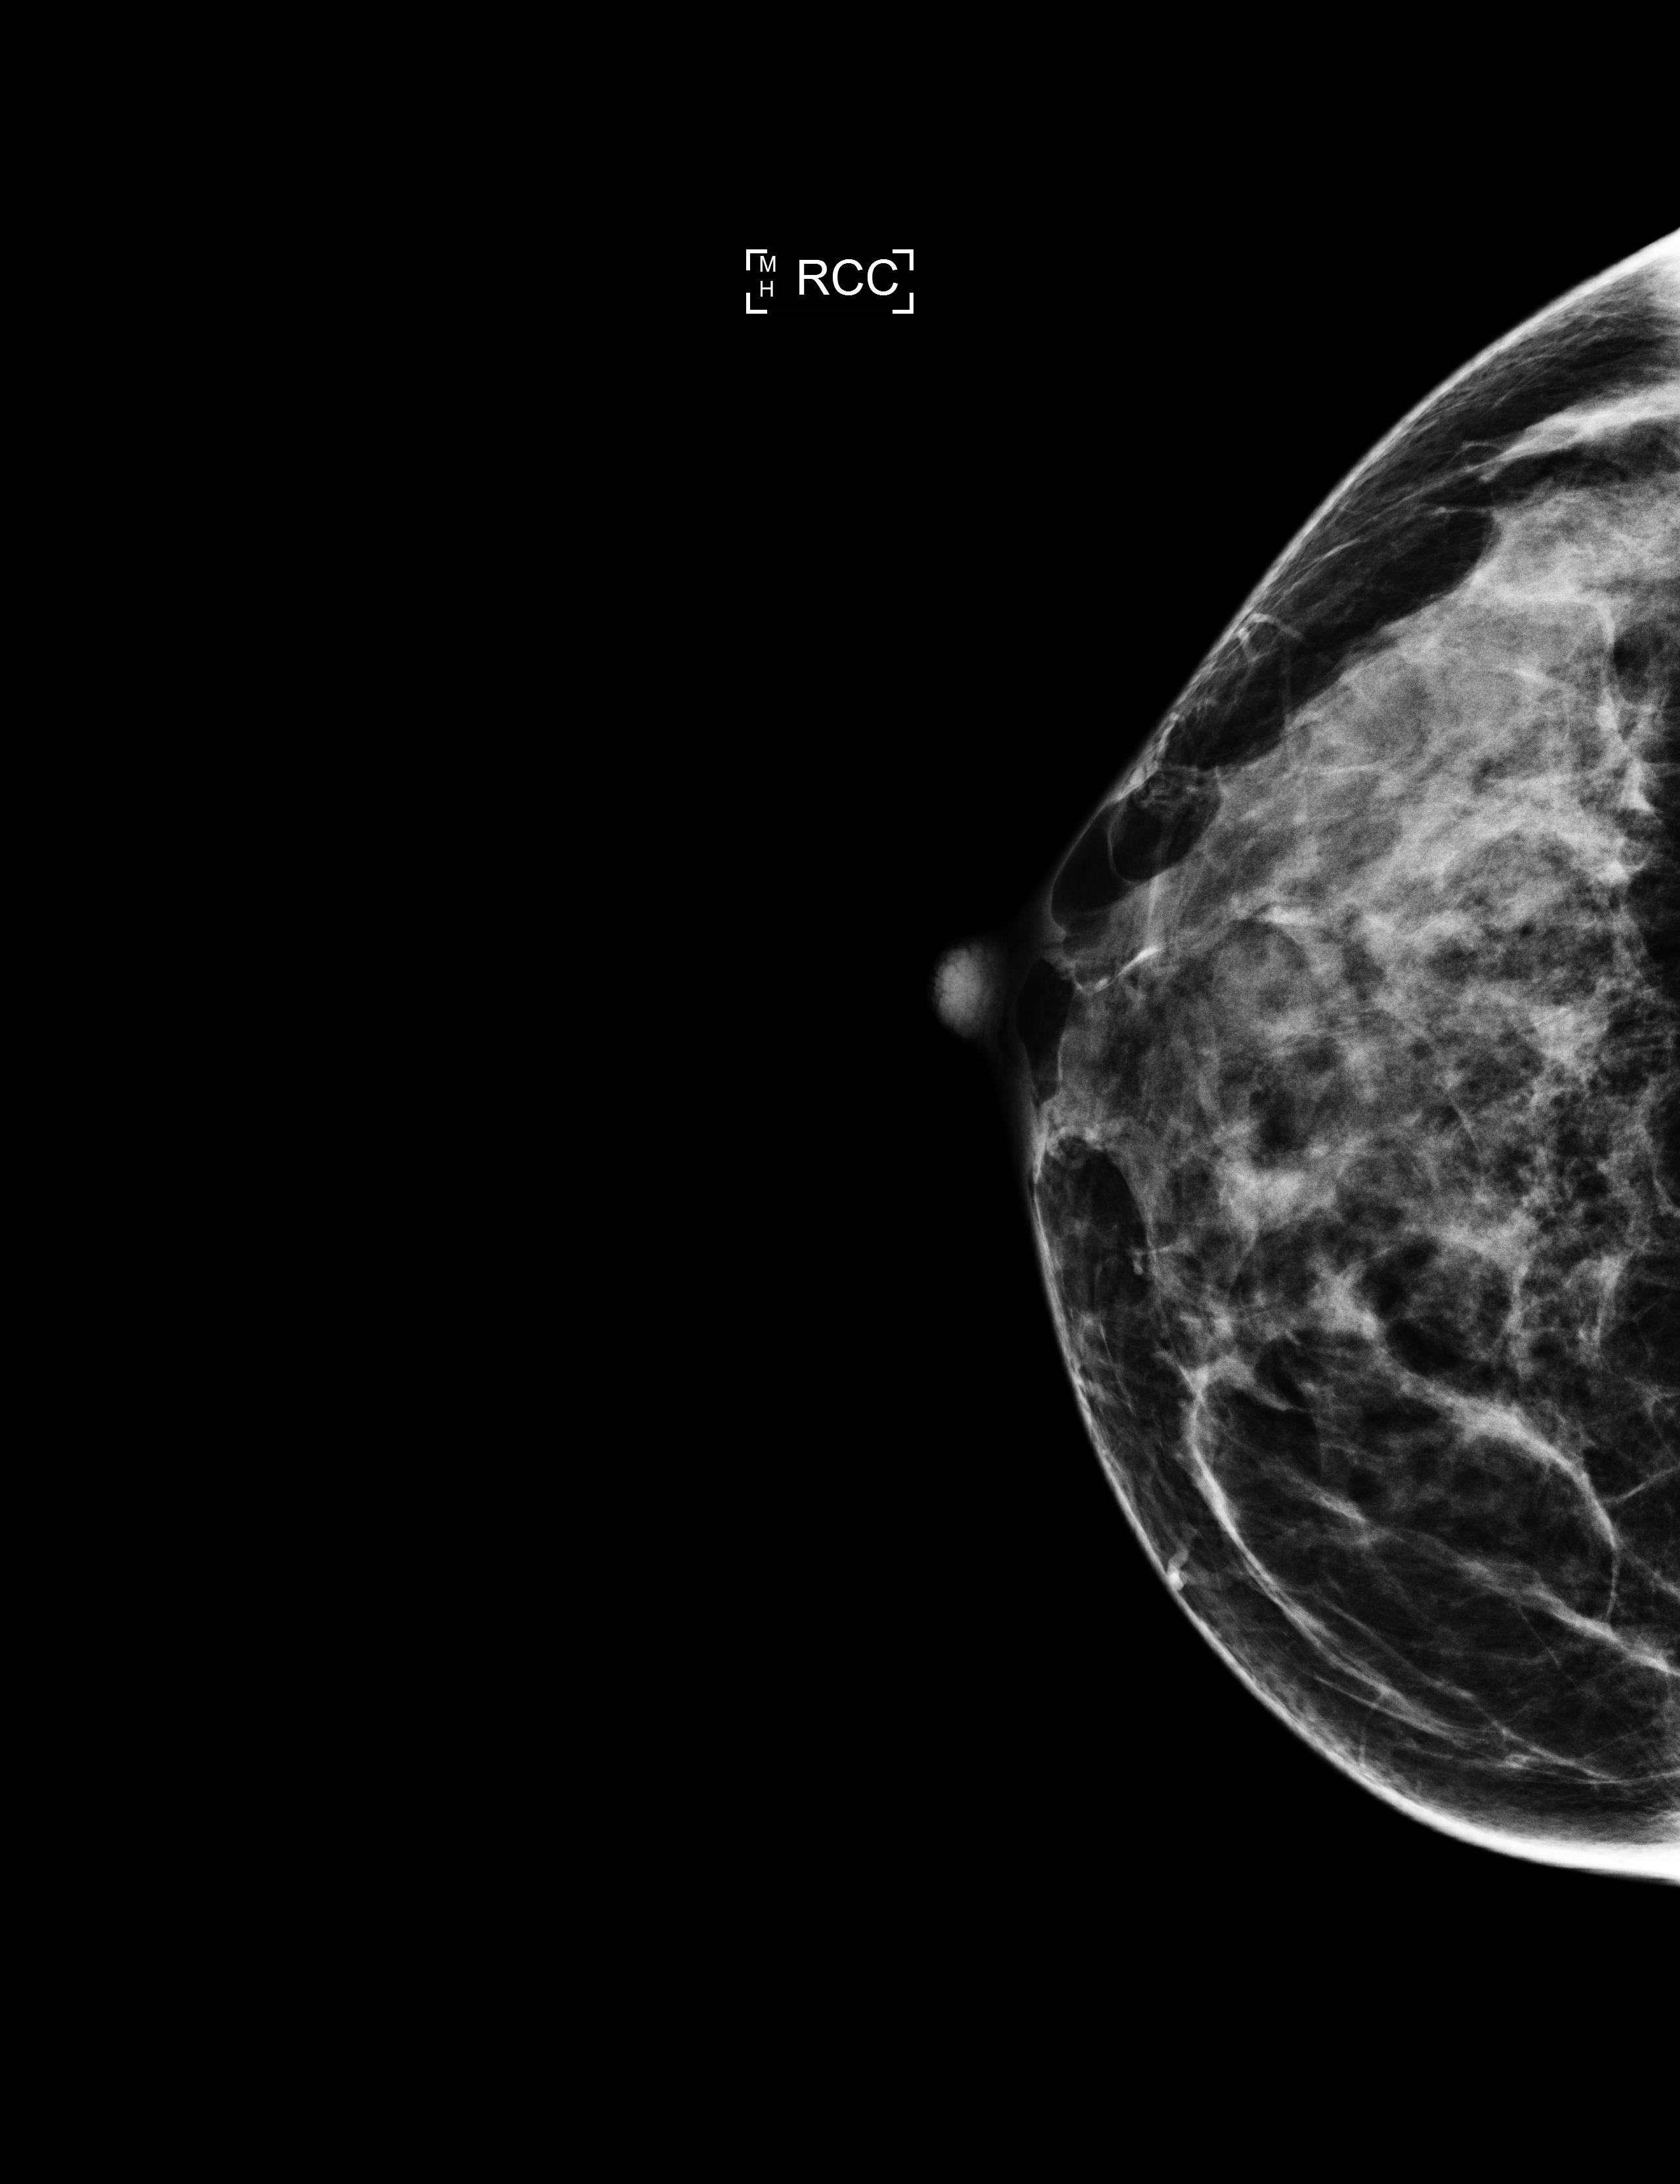
Screening examination. Patient: female, 41 years.
Image type: full-field digital mammogram. Breast: right. Projection: cranio-caudal projection. BI-RADS breast density category at the screening exam (both breasts, scale 1–4): 4. Final BI-RADS category for the screening round (tomosynthesis exam, both breasts): category 1. Recall: no recall after this screen.